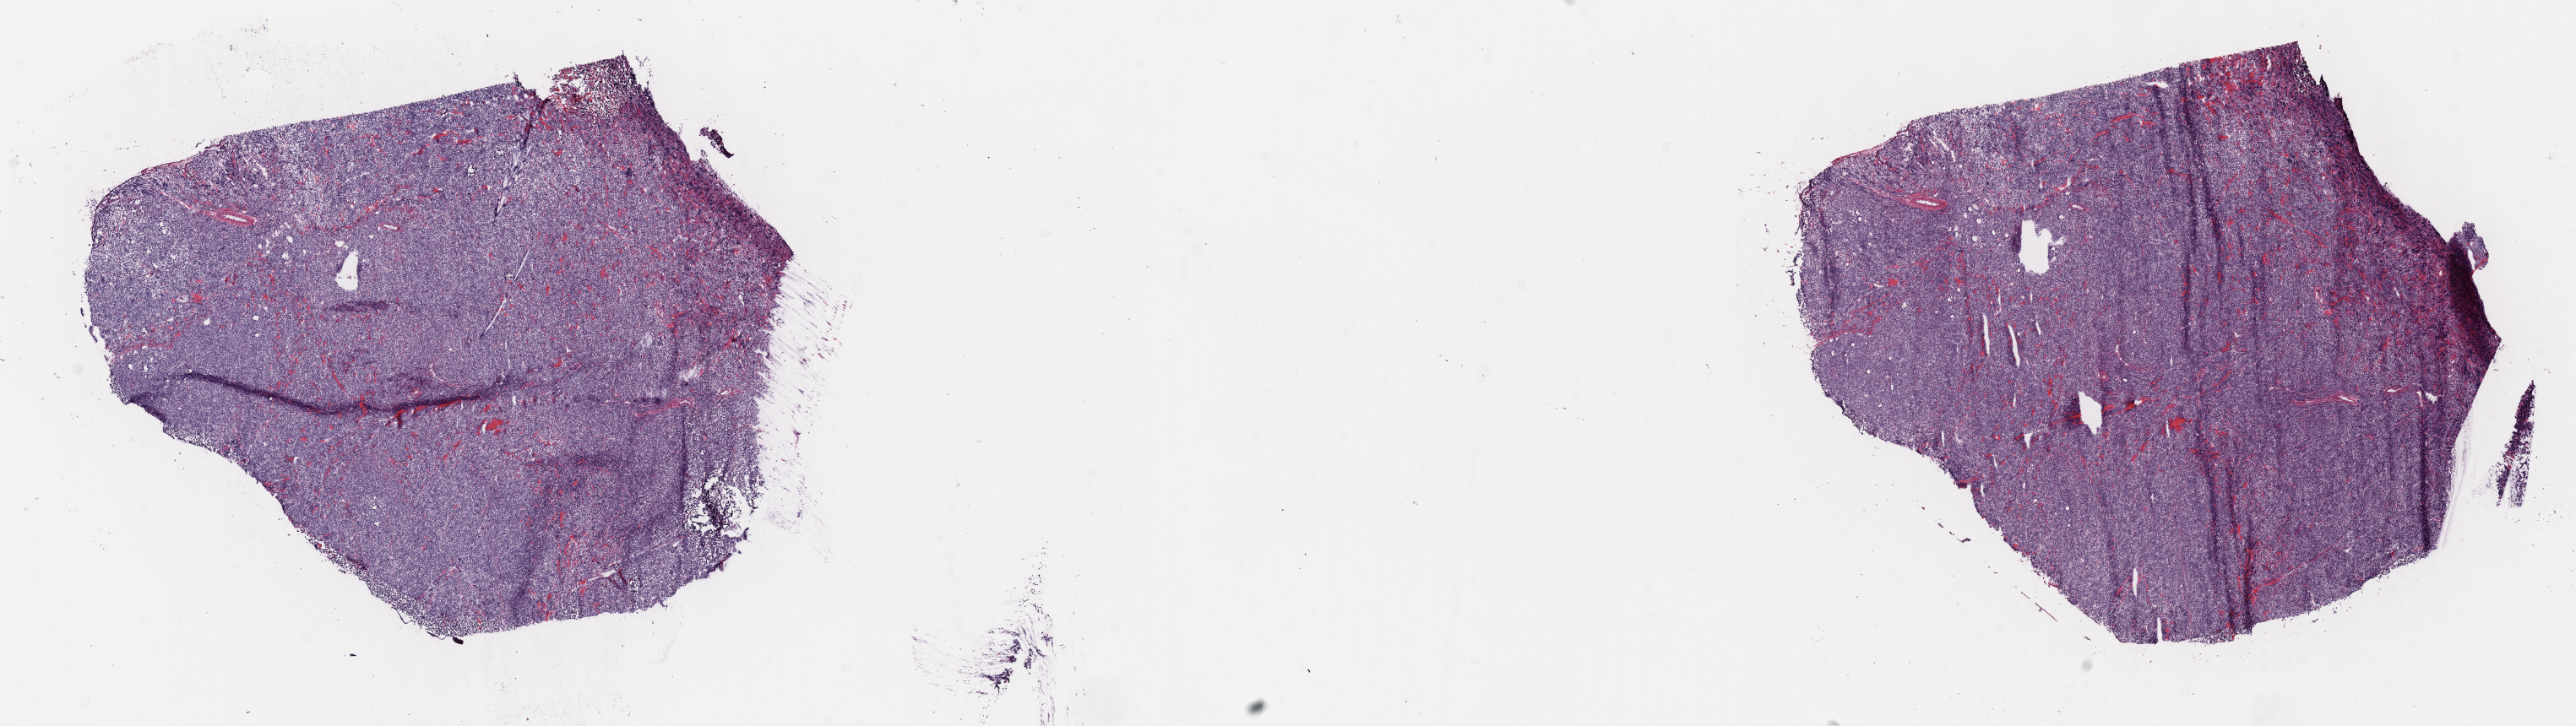
Digitized haematoxylin and eosin-stained section, whole scanned area (about 24.7 x 7.0 mm) shown as a low-resolution overview. Frozen section (tissue freezing medium). Specimen: primary tumor. Anatomic site: cranium. Patient: female, age at initial diagnosis 5 years. Pathologist review of this section (percent, as recorded): tumor cells 94%, tumor nuclei 95%, stromal cells 3%, necrosis 3%, normal cells 0%. Infiltration values recorded for this section: lymphocyte infiltration 2%, monocyte infiltration 3%, neutrophil infiltration 0%.
* section: bottom of the tissue portion
* Ann Arbor stage (patient): Stage IV
* diagnosis: Burkitt lymphoma, NOS